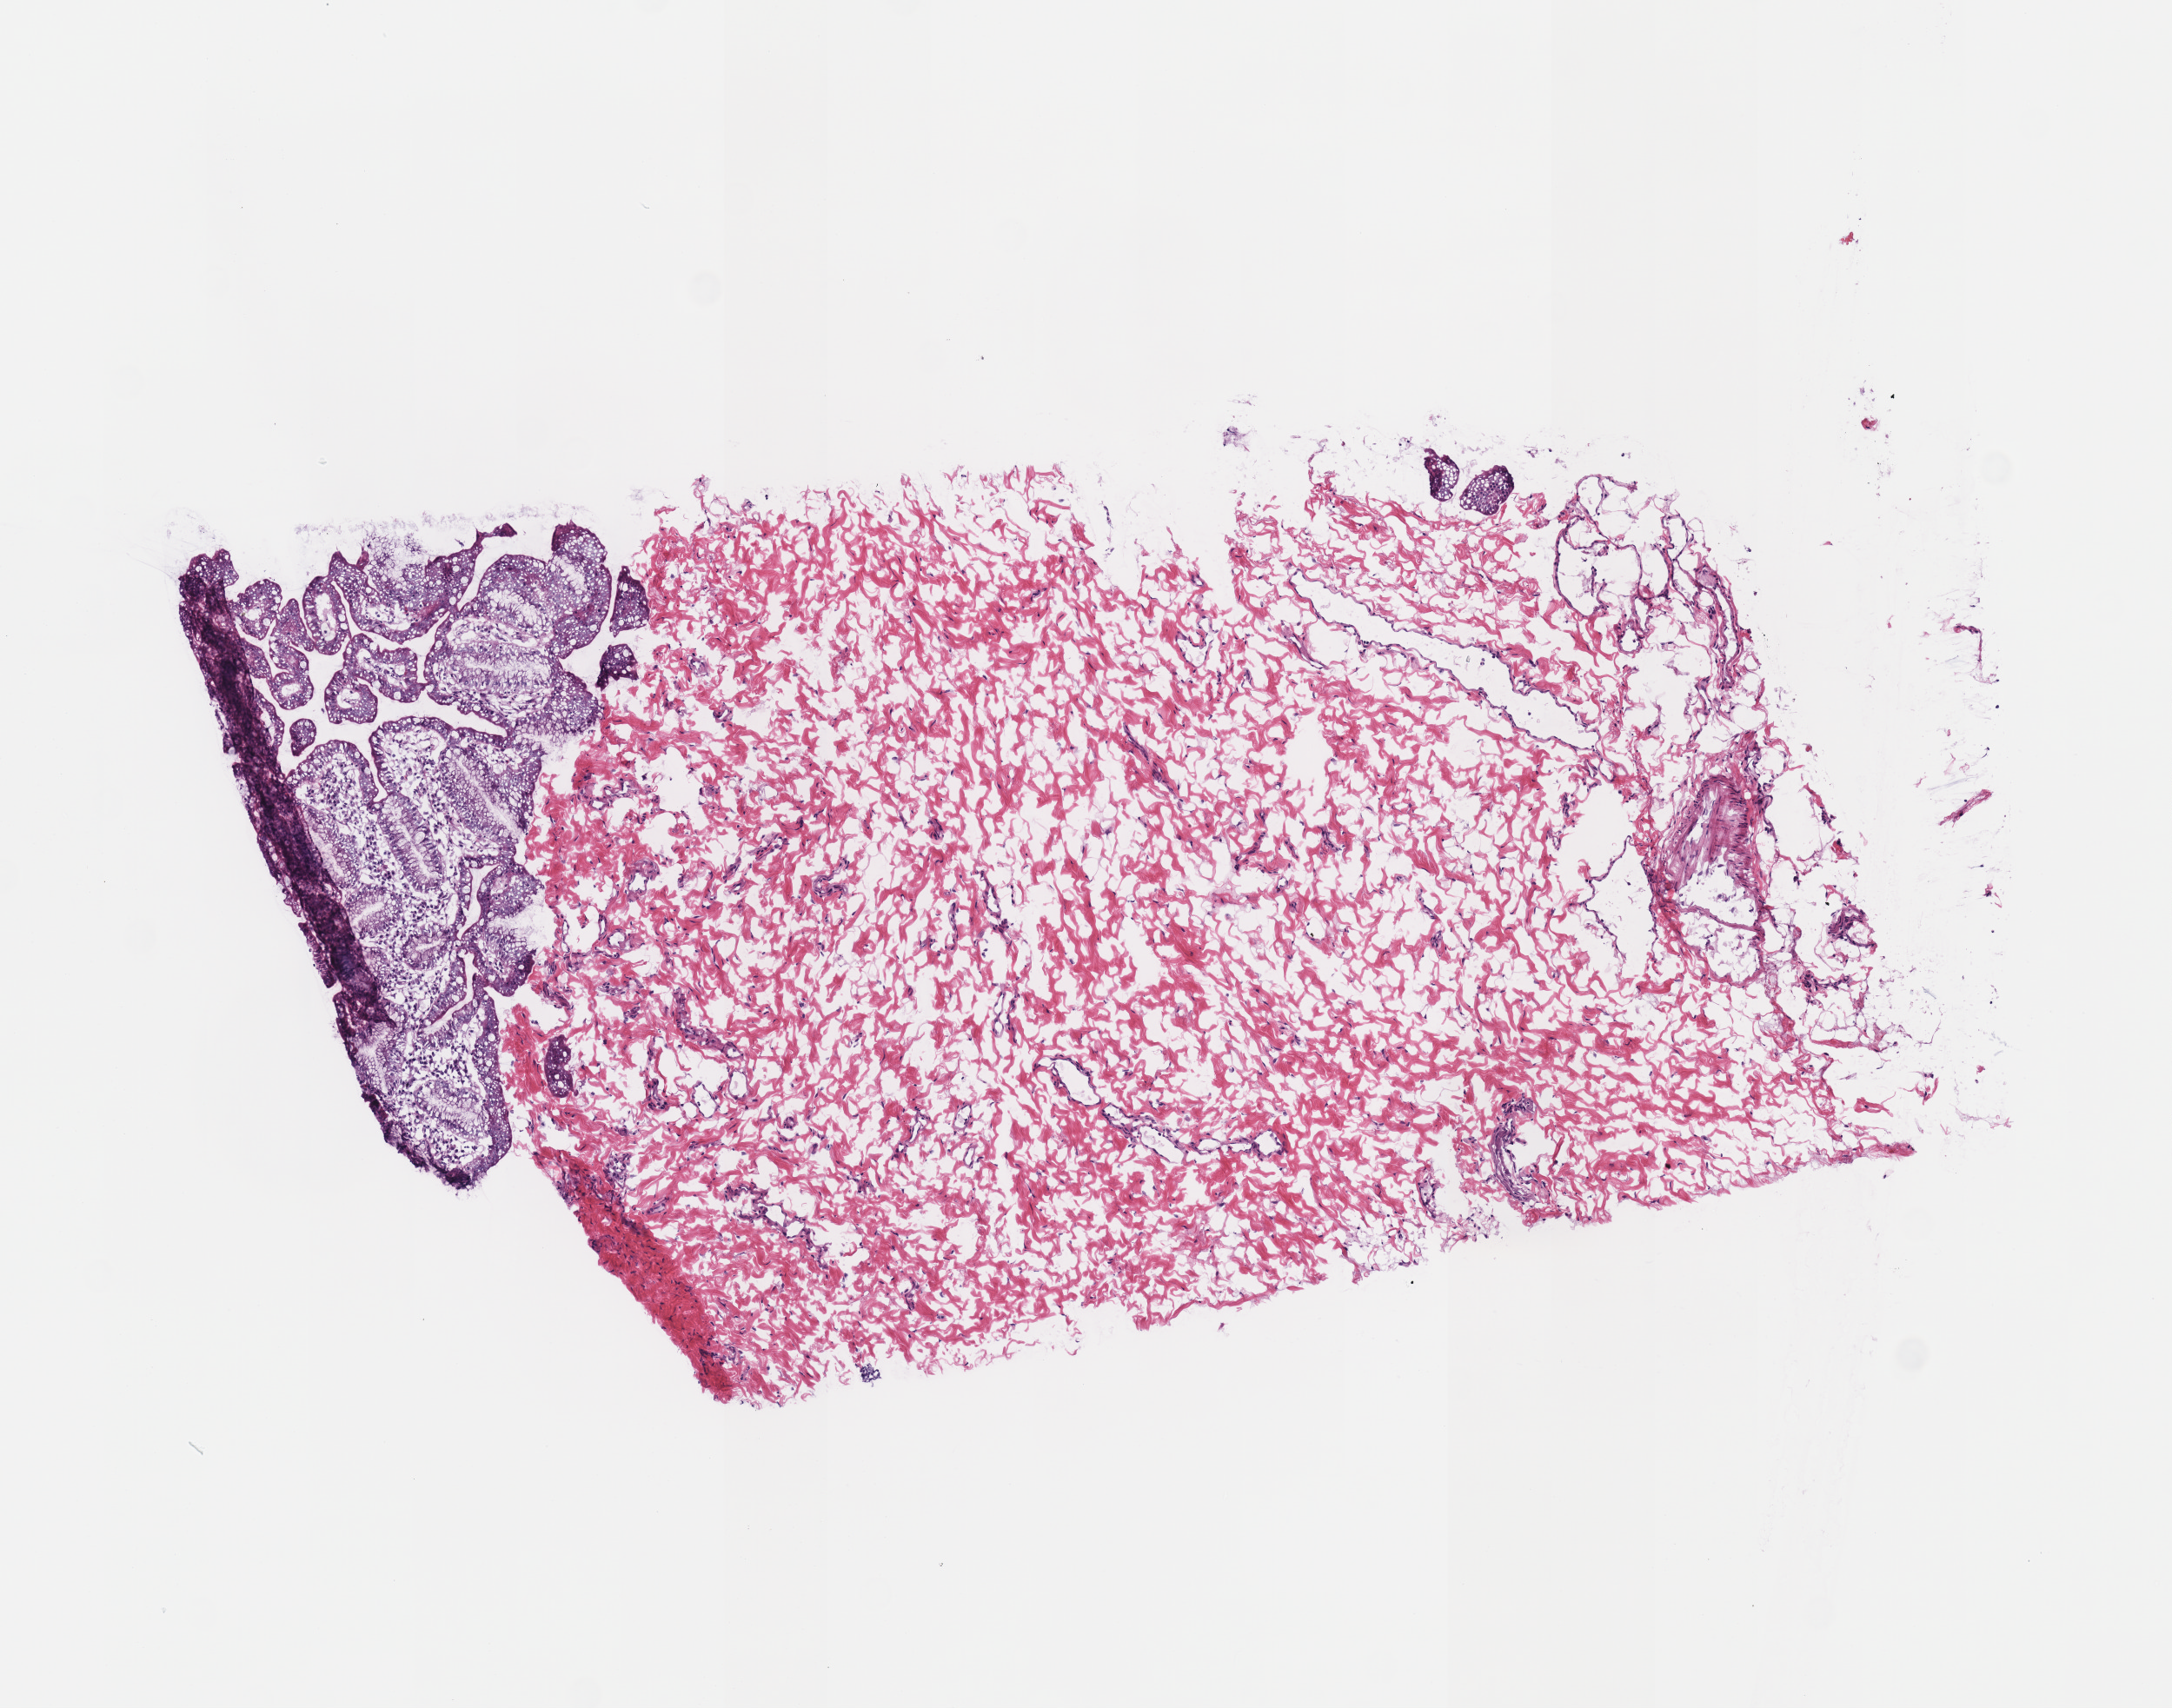
Digitized H&E tissue section (whole slide) — shown as a low-resolution overview of the whole scanned area (about 4.9 x 3.9 mm, from a 40x scan). Frozen section from the top of the tissue portion. Sample: solid tissue normal (non-tumour tissue), stomach. Male patient; age at initial diagnosis 56 years.
This section: solid tissue normal sample (biorepository sample class). Patient diagnosis: Tubular adenocarcinoma.